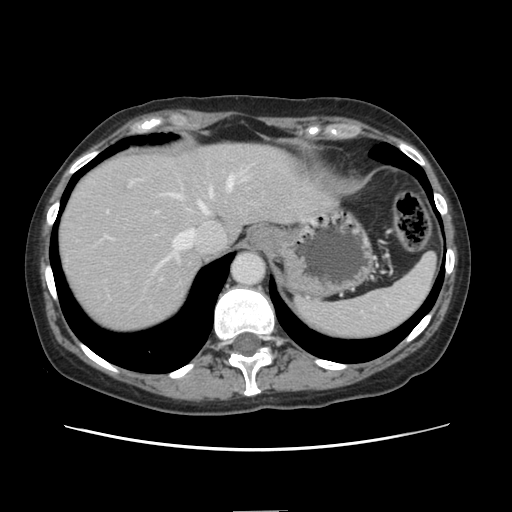
Contrast-enhanced abdominal CT, one axial slice. Slice 115 of 141 in the series (ordered by position). 120 kVp. Intravenous contrast given. Soft-tissue window (W 400 / L 40 HU). 512 × 512 image matrix. Female patient, age 63 years. From the clinical record (not read from this slice): diagnosis: colorectal cancer liver metastases, imaged before liver resection; multiple liver metastases: yes; largest metastasis: 3.2 cm.
Structures marked on this image (expert manual segmentation):
- hepatic veins: box from (x=154, y=177) to (x=234, y=273) px
- liver: (x=58, y=143)–(x=333, y=334)
- planned liver remnant (the part of the liver to remain after resection): (x=198, y=144)–(x=330, y=238)
- portal vein (with intrahepatic branches): (x=167, y=171)–(x=245, y=204)